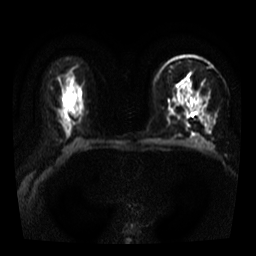
Breast MRI, one axial slice. Diffusion-weighted series; image 2 of 4 stored at this slice position (different b-values; order by instance number). 3 T. 5 mm slice thickness. 256 × 256 image matrix, field of view 320 × 320 mm. Female patient.
Outlined on this slice (manually delineated by an expert):
- tumour on diffusion-weighted imaging: bounding box (x1, y1, x2, y2) in pixels: (185, 111, 191, 117)